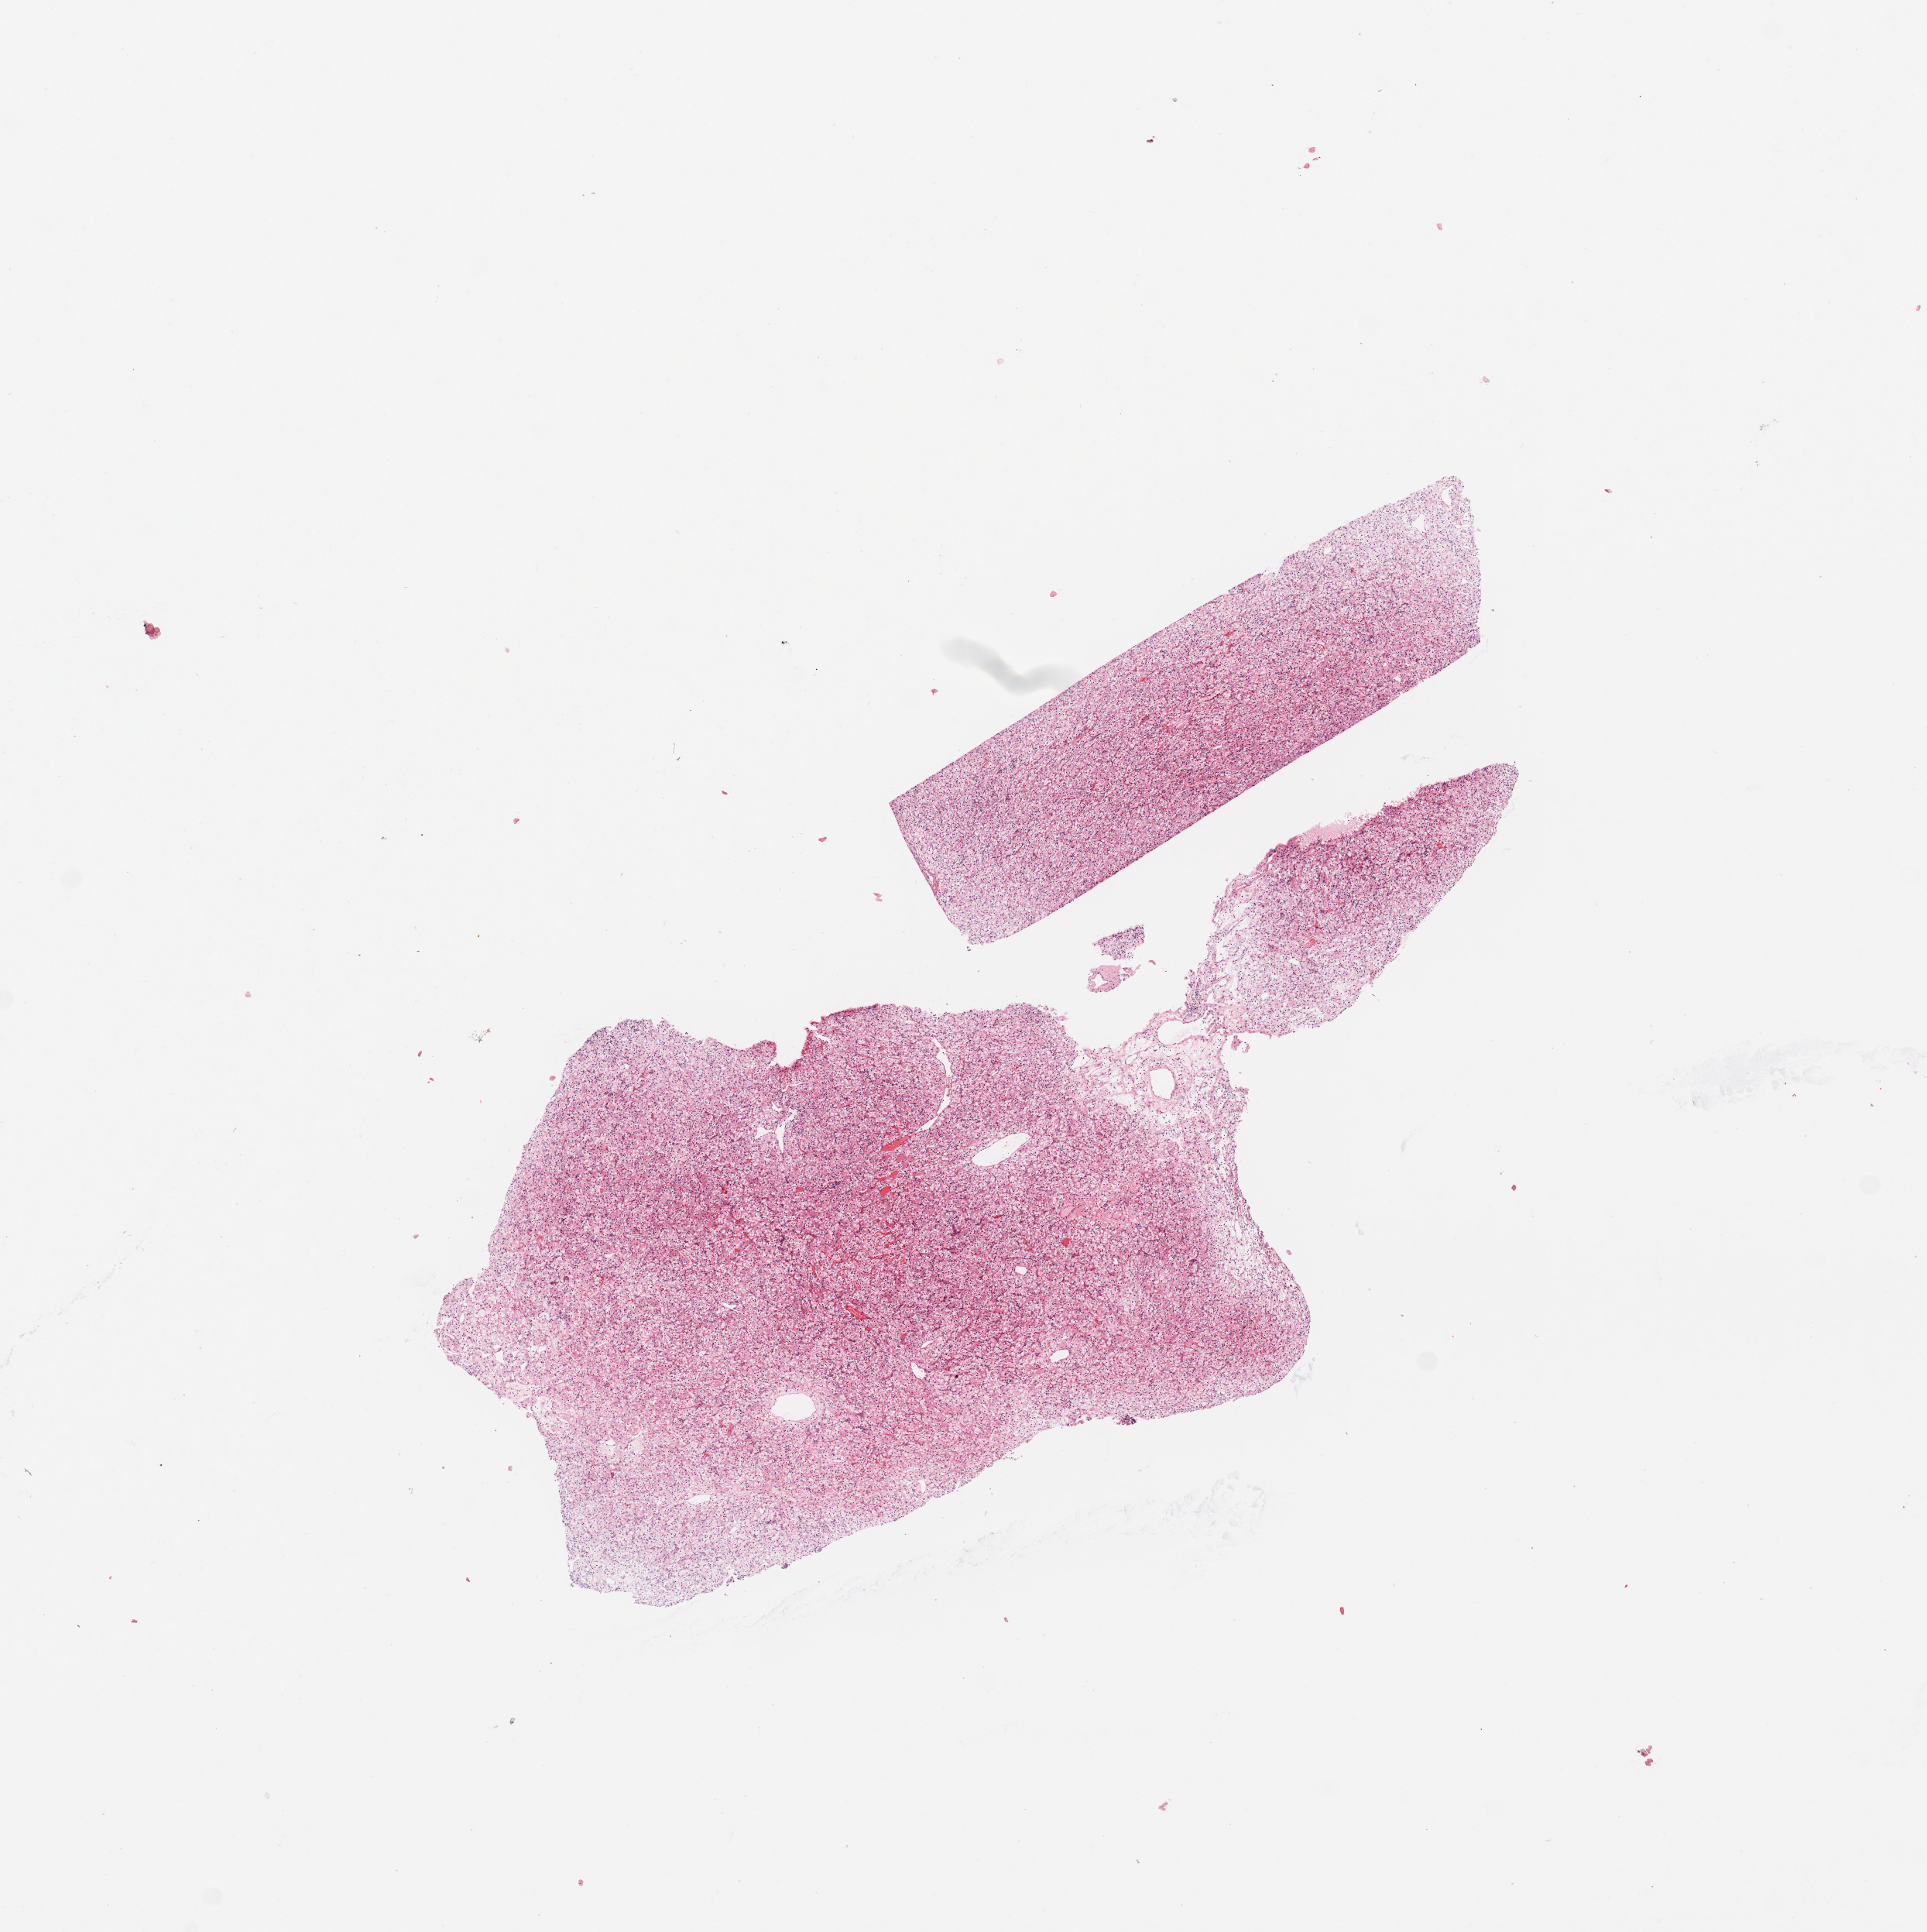
Whole-slide histology image, H&E-stained, whole scanned area (about 9.8 x 9.9 mm, from a 20x scan) shown as a low-resolution overview; tumour tissue sample, sampled site: kidney. Male, 63 y/o. Histologic grade: G2 (moderately differentiated). Pathologist review of this section (percent, as recorded): tumour nuclei 85%, necrosis 2%.
- primary tumour site (as recorded): lower pole
- histologic diagnosis: Renal cell carcinoma, NOS
- AJCC pathologic stage: I